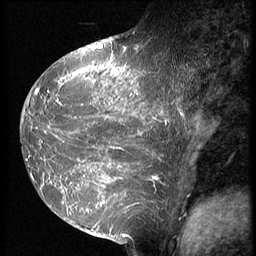
Breast MRI (dynamic contrast-enhanced), one sagittal slice. 3 images stored at this slice position (order not interpretable as contrast timing). 1.5 T. TE 4.2 ms, TR 9 ms. 2.5 mm slice thickness. 256 × 256 image matrix. Female patient, age 39 years. Case-level facts recorded for this patient, not image findings: setting: breast cancer imaged before/during neoadjuvant chemotherapy; receptor status: HER2-positive.
Structures marked on this image (semi-automatically segmented with operator editing):
- analysis volume of interest (the breast-tissue region the enhancement analysis was run in; not a lesion): bounding box (x1, y1, x2, y2) in pixels: (23, 47, 182, 239)
- tumour enhancement mask (voxels above the 140 % enhancement threshold inside the analysis volume of interest): (23, 47, 181, 238)